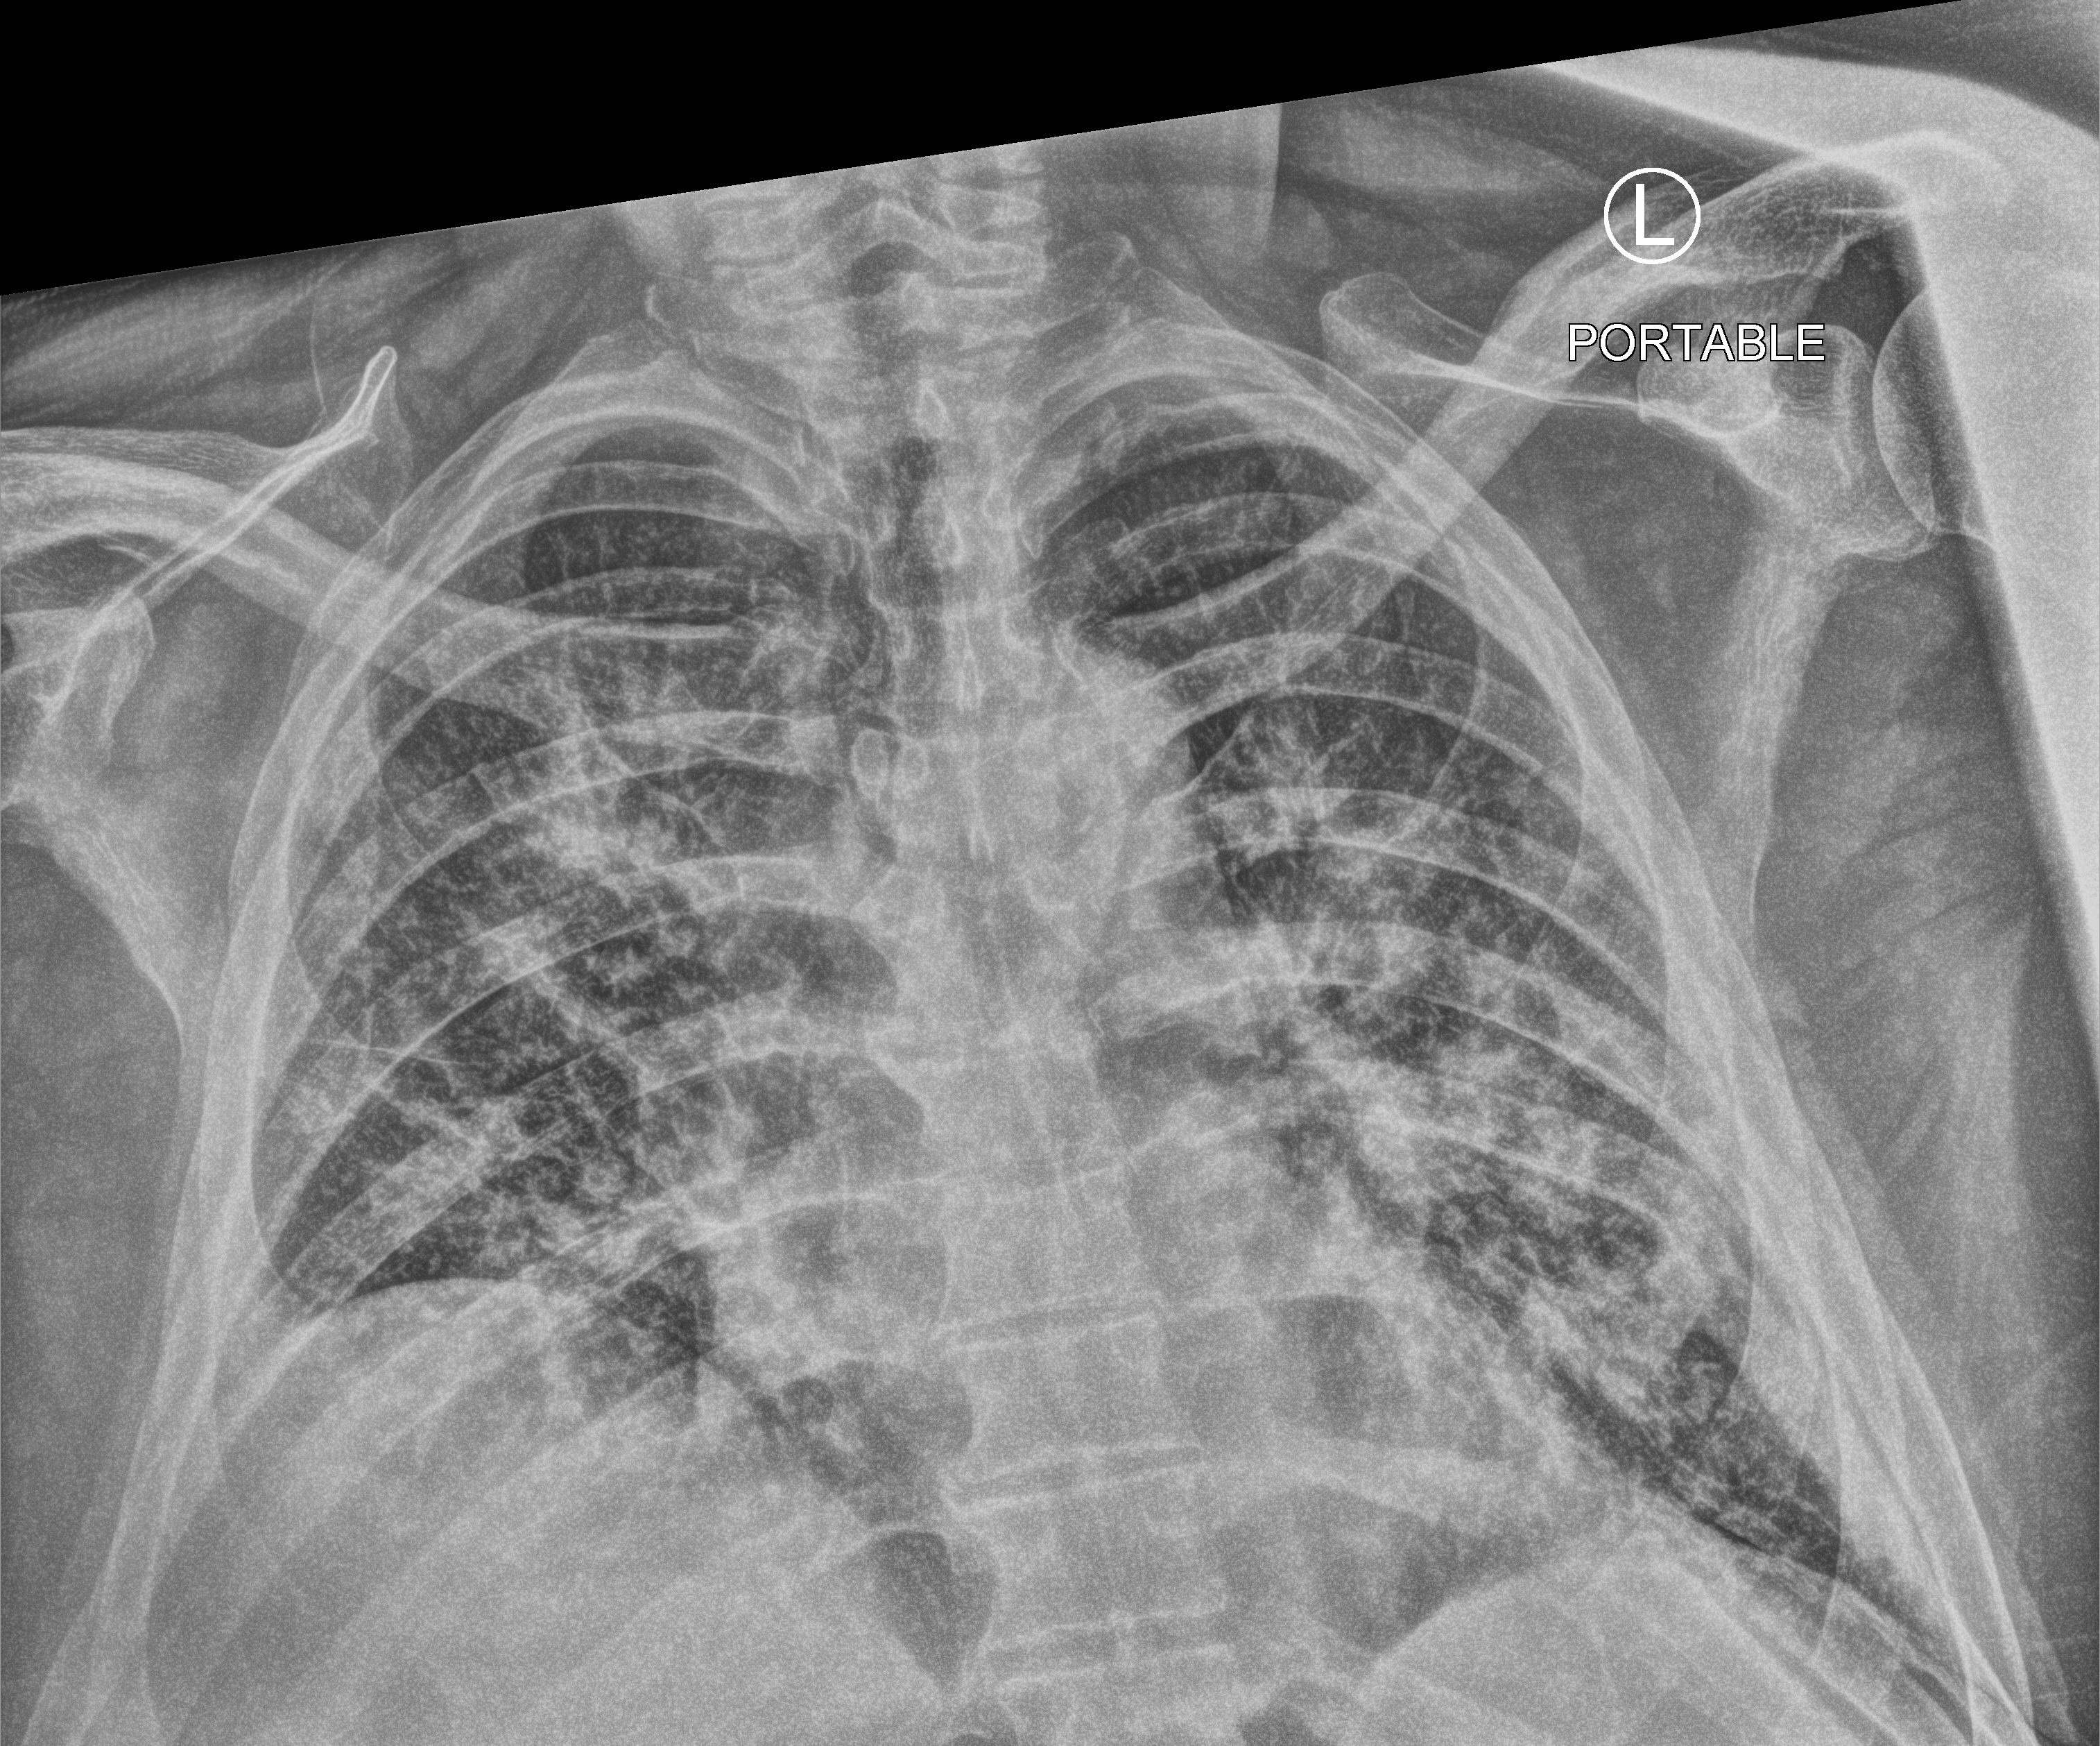
Bedside chest radiograph (computed radiography); anteroposterior (AP) projection. Patient hospitalised with COVID-19; male, aged 60–74 years.
Admission-level facts for this patient (not findings on this image; timing relative to this image not recorded):
- mechanically ventilated during this hospital stay: no
- hypertension (admission record): yes